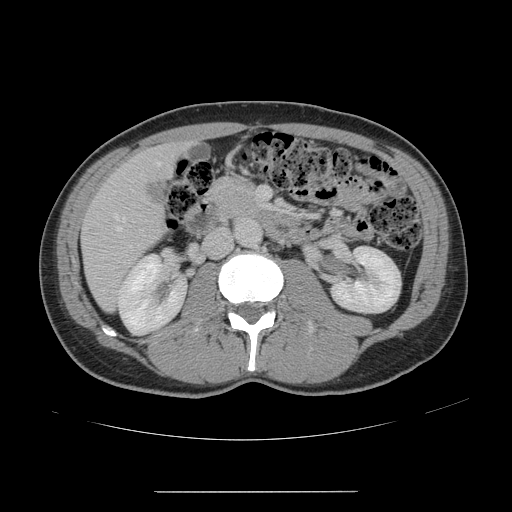
Contrast-enhanced abdominal CT, one axial slice; position 56 of 178 along the scan axis; intravenous contrast given; soft-tissue window (W 400 / L 40 HU); 2.5 mm slice thickness; 512 × 512 image matrix, field of view 401 × 401 mm. Male patient, age 53 years. Case-level facts recorded for this patient, not image findings: diagnosis: colorectal cancer liver metastases, imaged before liver resection; multiple liver metastases: yes; largest metastasis: 2.4 cm; disease in both lobes: no.
Structures marked on this image (outlined manually by an expert reader):
- hepatic veins: bounding box [x1, y1, x2, y2] px = [111, 162, 160, 247]
- liver: [82, 145, 183, 309]
- portal vein (with intrahepatic branches): [257, 187, 267, 207]
- liver metastasis: [145, 180, 165, 204]